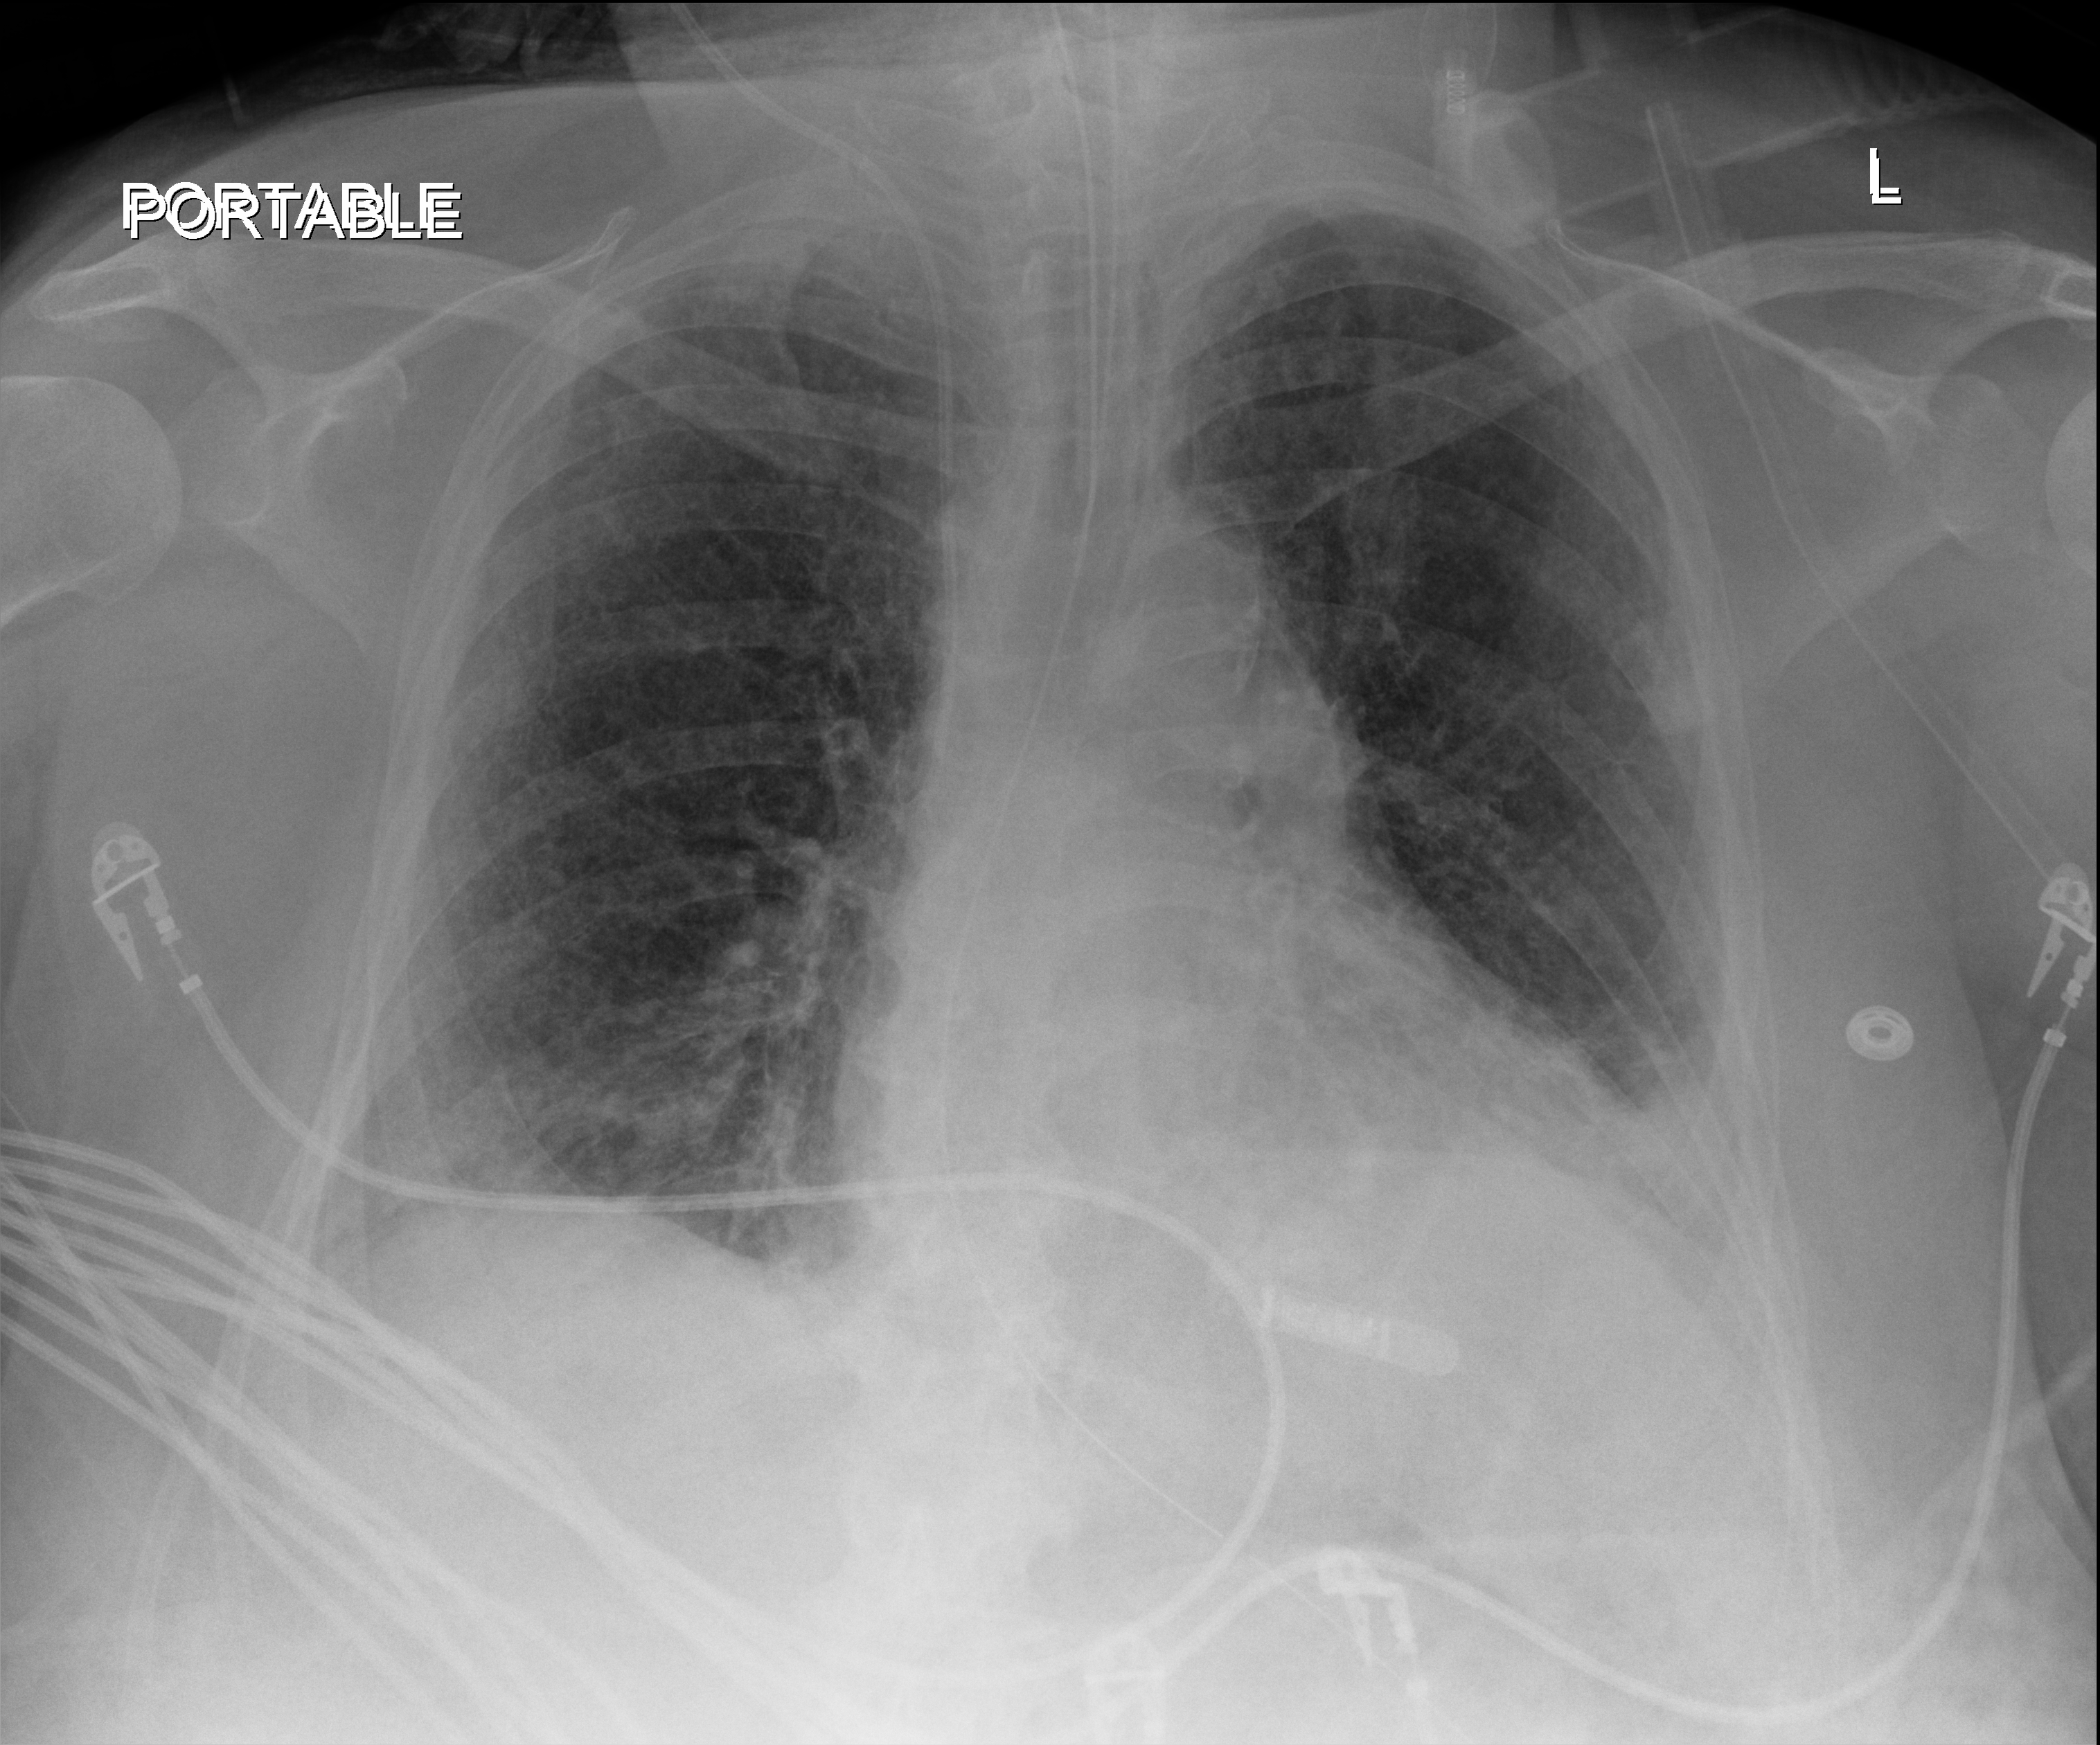
Portable chest radiograph, anteroposterior (AP) projection. Female patient hospitalised with COVID-19, age 60–74 years.
Admission-level facts for this patient (not findings on this image; timing relative to this image not recorded):
- hypertension (admission record): yes